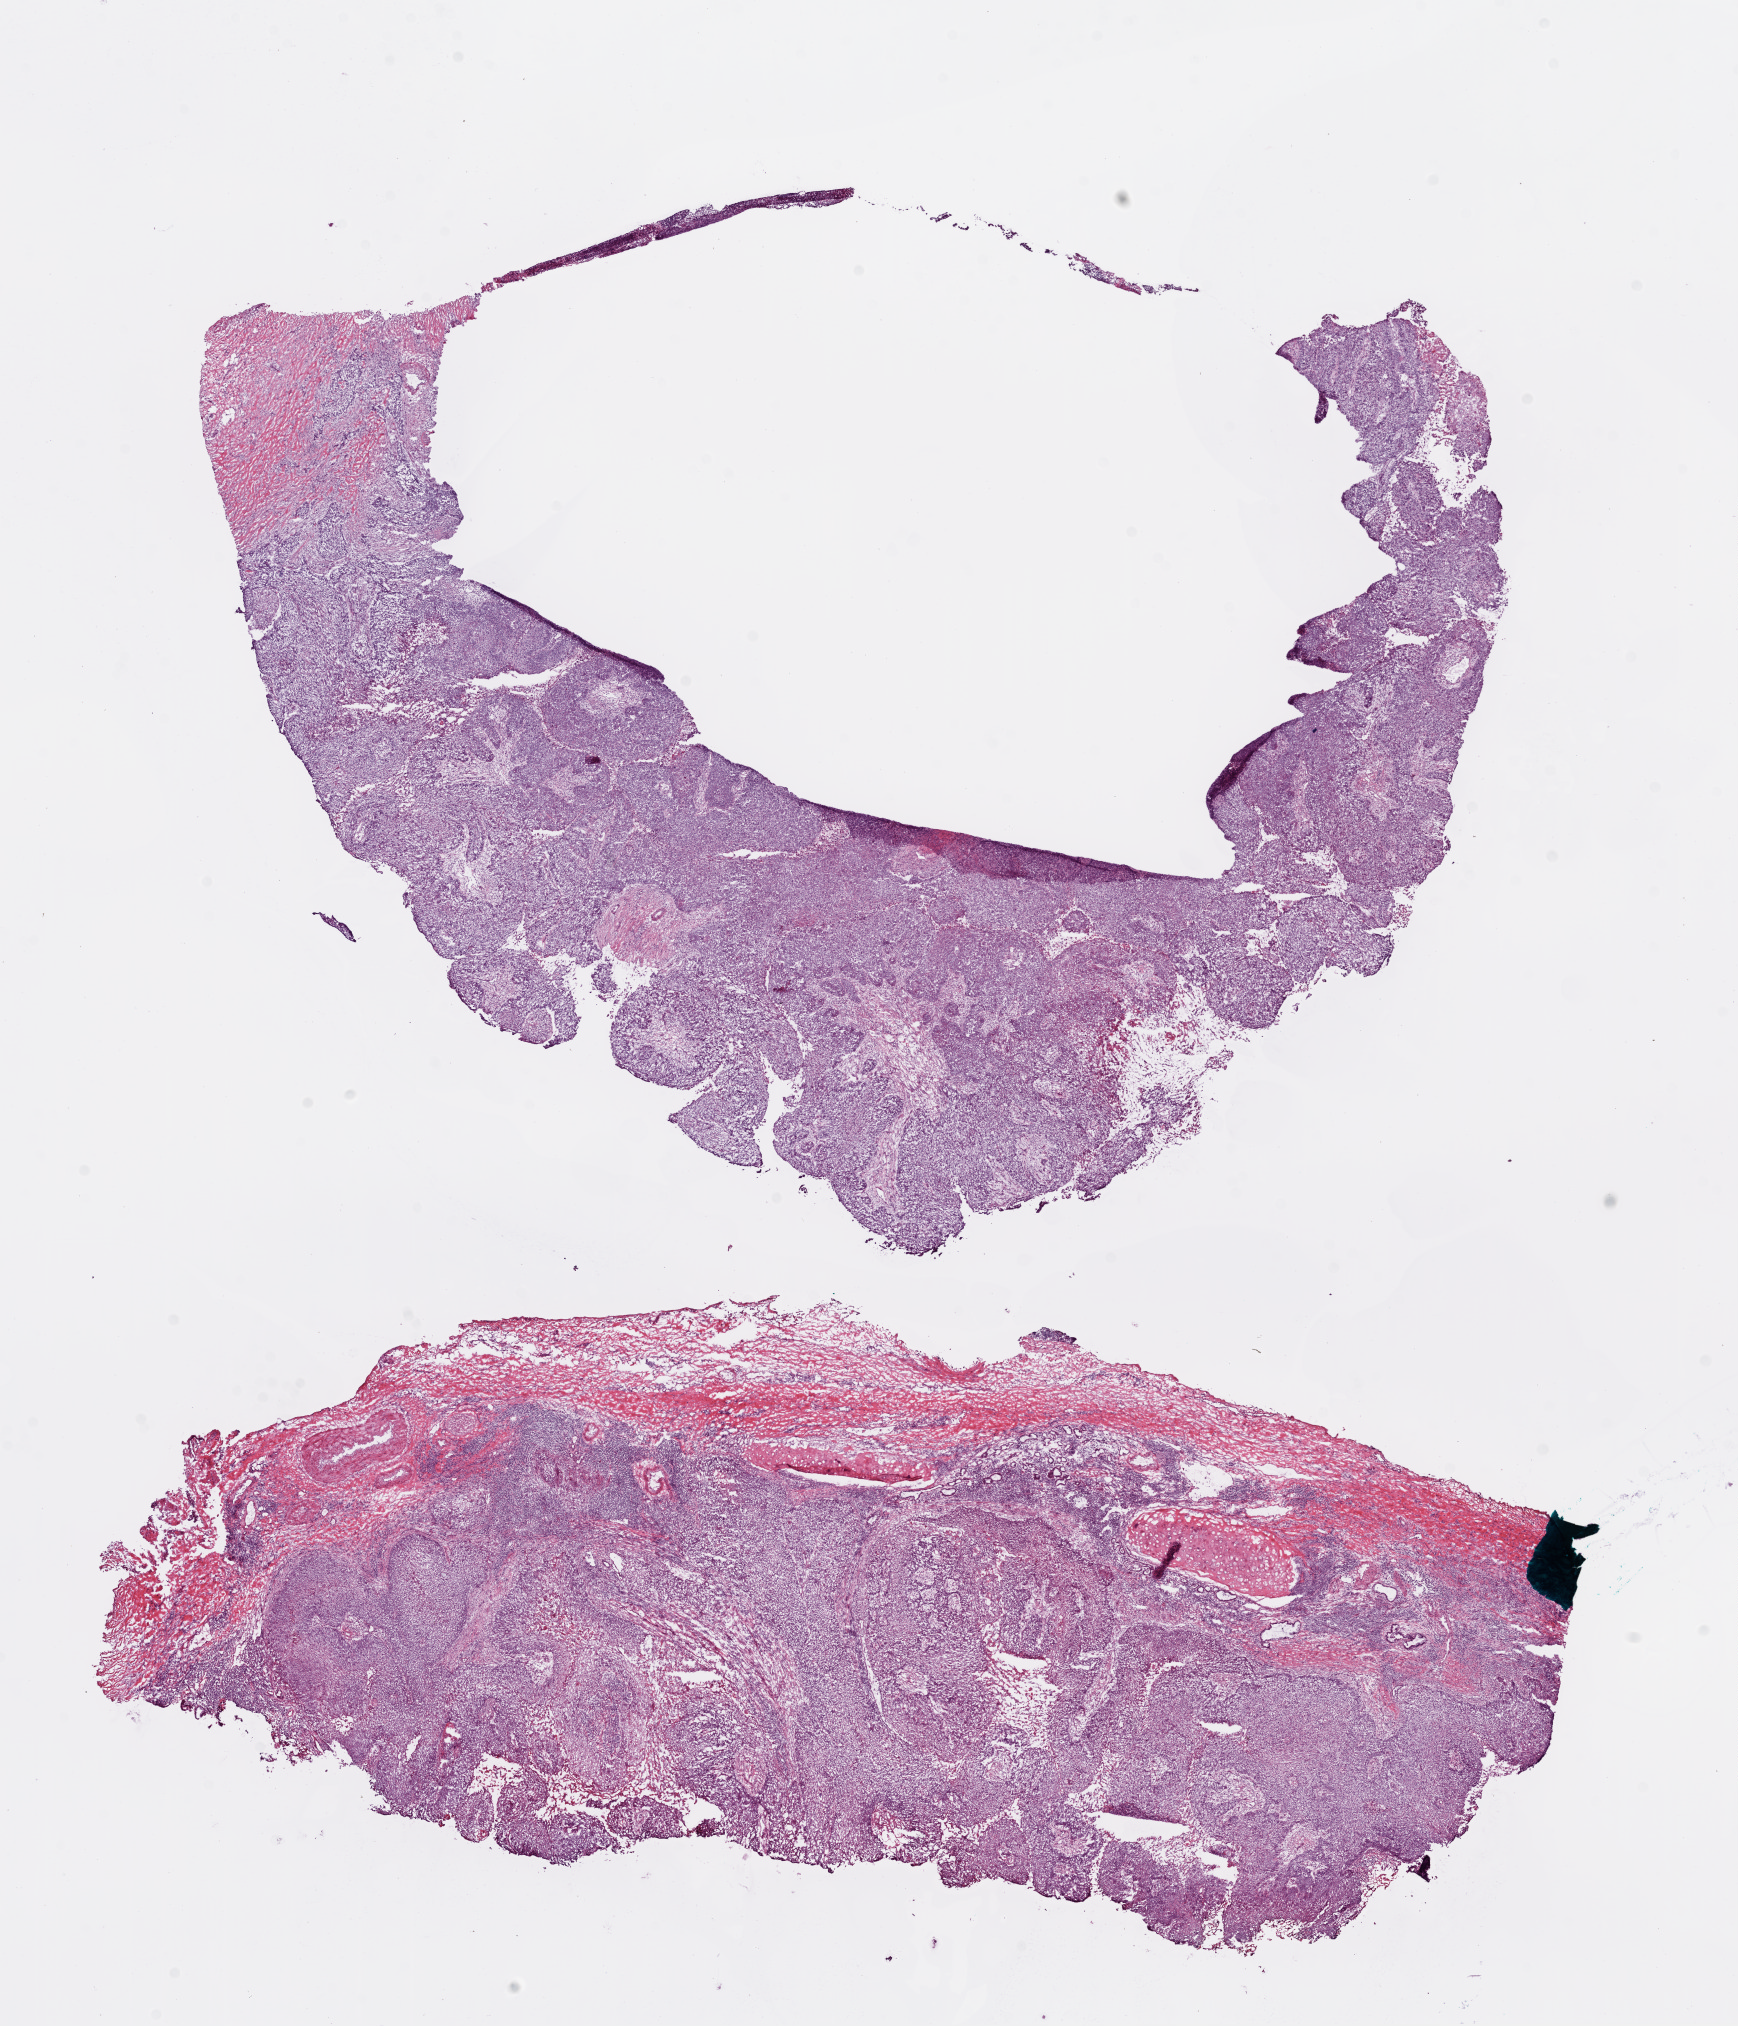
H&E-stained whole-slide image, shown as a low-resolution overview of the whole scanned area (about 14.0 x 16.3 mm, slide scanned at 20x), frozen section from the bottom of the tissue portion, primary tumour sample from the lung. Male patient; age at initial diagnosis 75 years. Composition of this section per pathologist review: tumour nuclei 95%, necrosis 10%.
Histologic diagnosis: Squamous cell carcinoma, NOS. AJCC pathologic stage: IB.